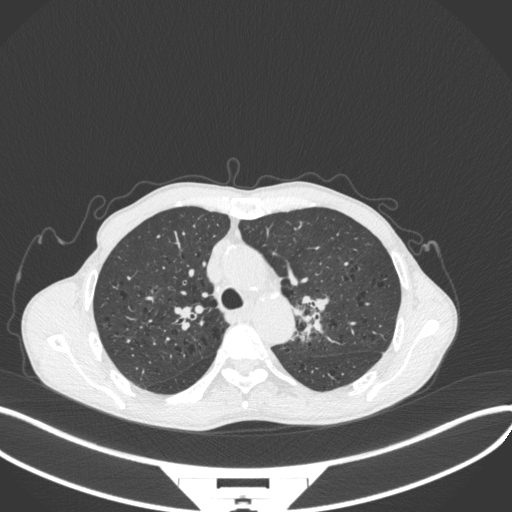
Chest CT, one axial slice. Slice 302 of 394 in the series (ordered by position). Reconstruction kernel B31f. Lung window (W 1500 / L -600 HU). 512 × 512 image matrix, field of view 400 × 400 mm. Patient: male, 65 years. Case-level facts recorded for this patient, not image findings: clinical TNM (as recorded): T2b N0 M0; histopathological grade: G2.
Outlined on this slice (rectangle marked by the reading radiologist):
- lung tumour (recorded histology: adenocarcinoma): bounding box (x1, y1, x2, y2) in pixels: (289, 291, 331, 350)